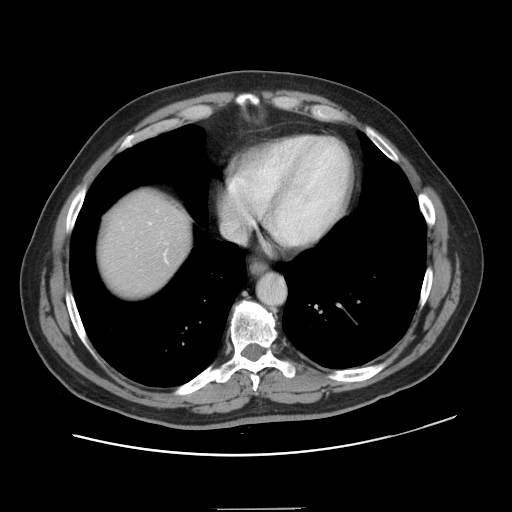
Contrast-enhanced abdominal CT, one axial slice. Position 136 of 143 along the scan axis. 120 kVp. Soft-tissue window (W 400 / L 40 HU). 2.5 mm slice thickness. 512 × 512 image matrix, field of view 402 × 402 mm. Male patient, age 62 years. From the clinical record (not read from this slice): diagnosis: colorectal cancer liver metastases, imaged before liver resection; multiple liver metastases: yes; largest metastasis: 2.7 cm; disease in both lobes: no.
Annotated regions visible in this slice (outlined manually by an expert reader):
- liver: bounding box [x1, y1, x2, y2] px = [101, 193, 189, 296]
- planned liver remnant (the part of the liver to remain after resection): [101, 193, 188, 296]